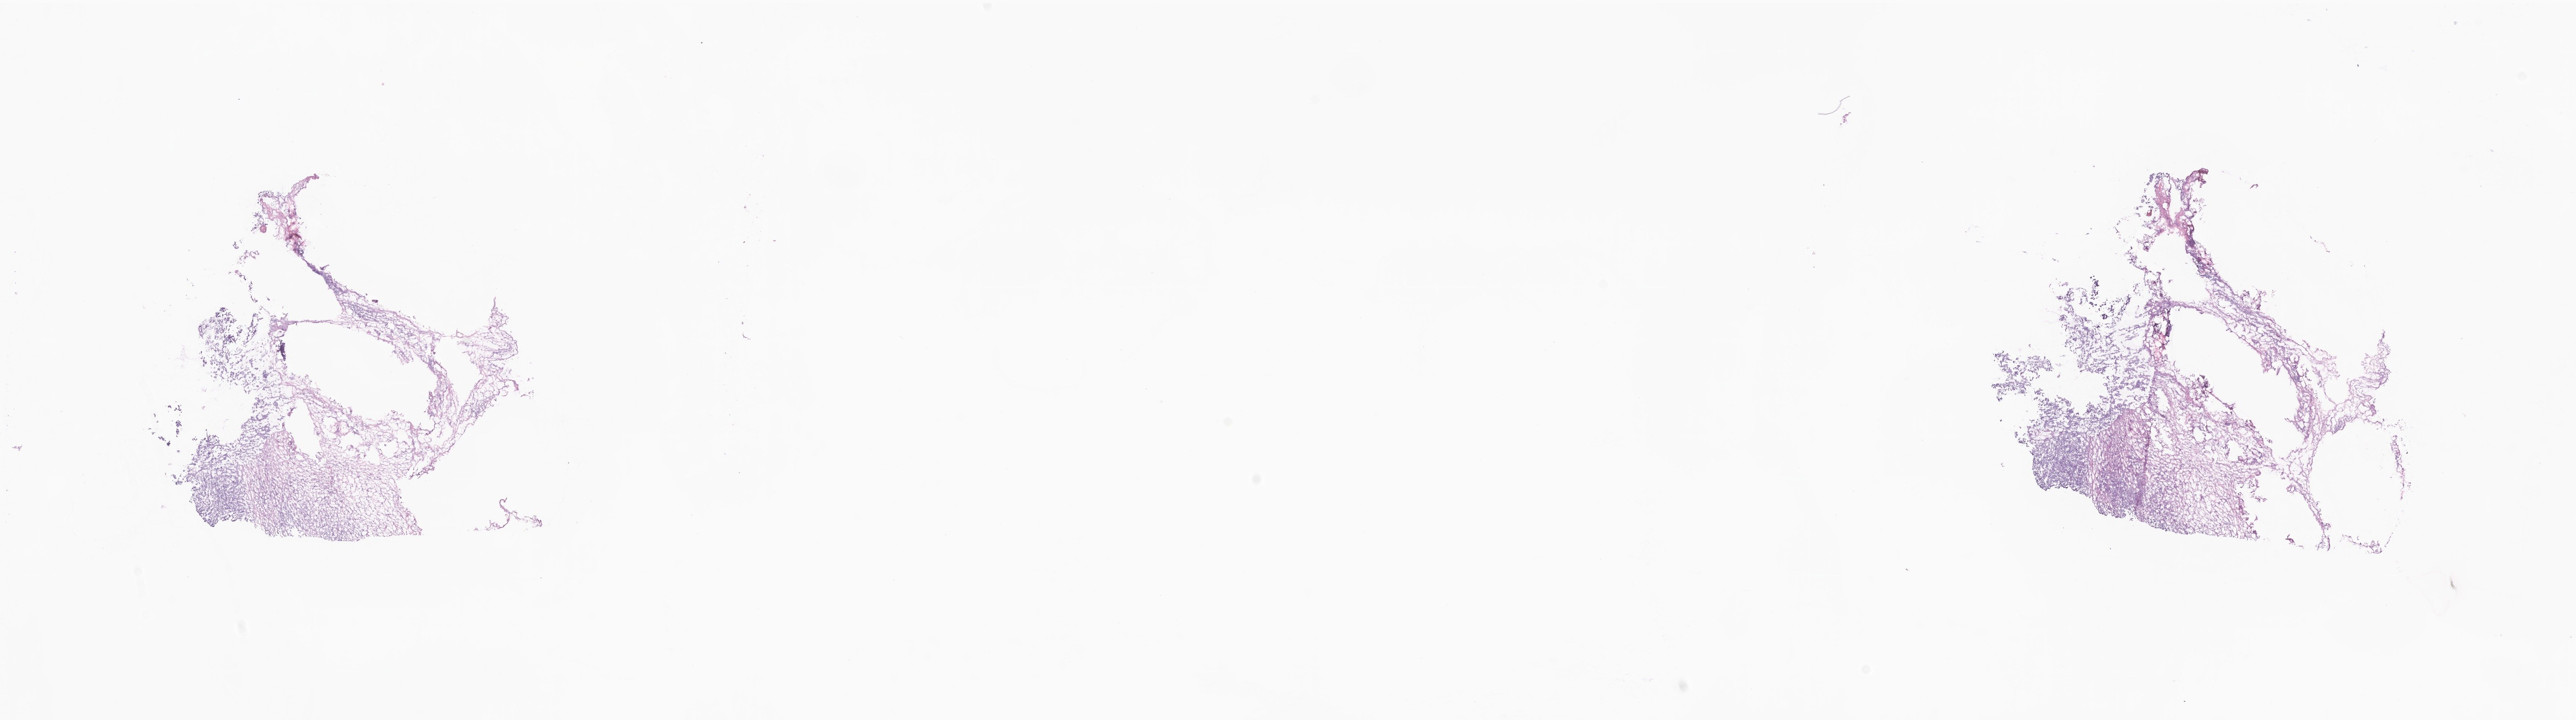
Digitized haematoxylin and eosin-stained section, whole scanned area (about 28.6 x 8.0 mm) shown as a low-resolution overview. Frozen section (tissue freezing medium). Metastatic tumor tissue. Female patient. Slide review estimates, as recorded: tumor cells 70%, tumor nuclei 67%, stromal cells 5%, necrosis 5%, normal cells 20%. Infiltration values recorded for this section: lymphocyte infiltration 0%, monocyte infiltration 0%, neutrophil infiltration 0%.
- patient diagnosis (primary): Serous surface papillary carcinoma
- section: top of the tissue portion